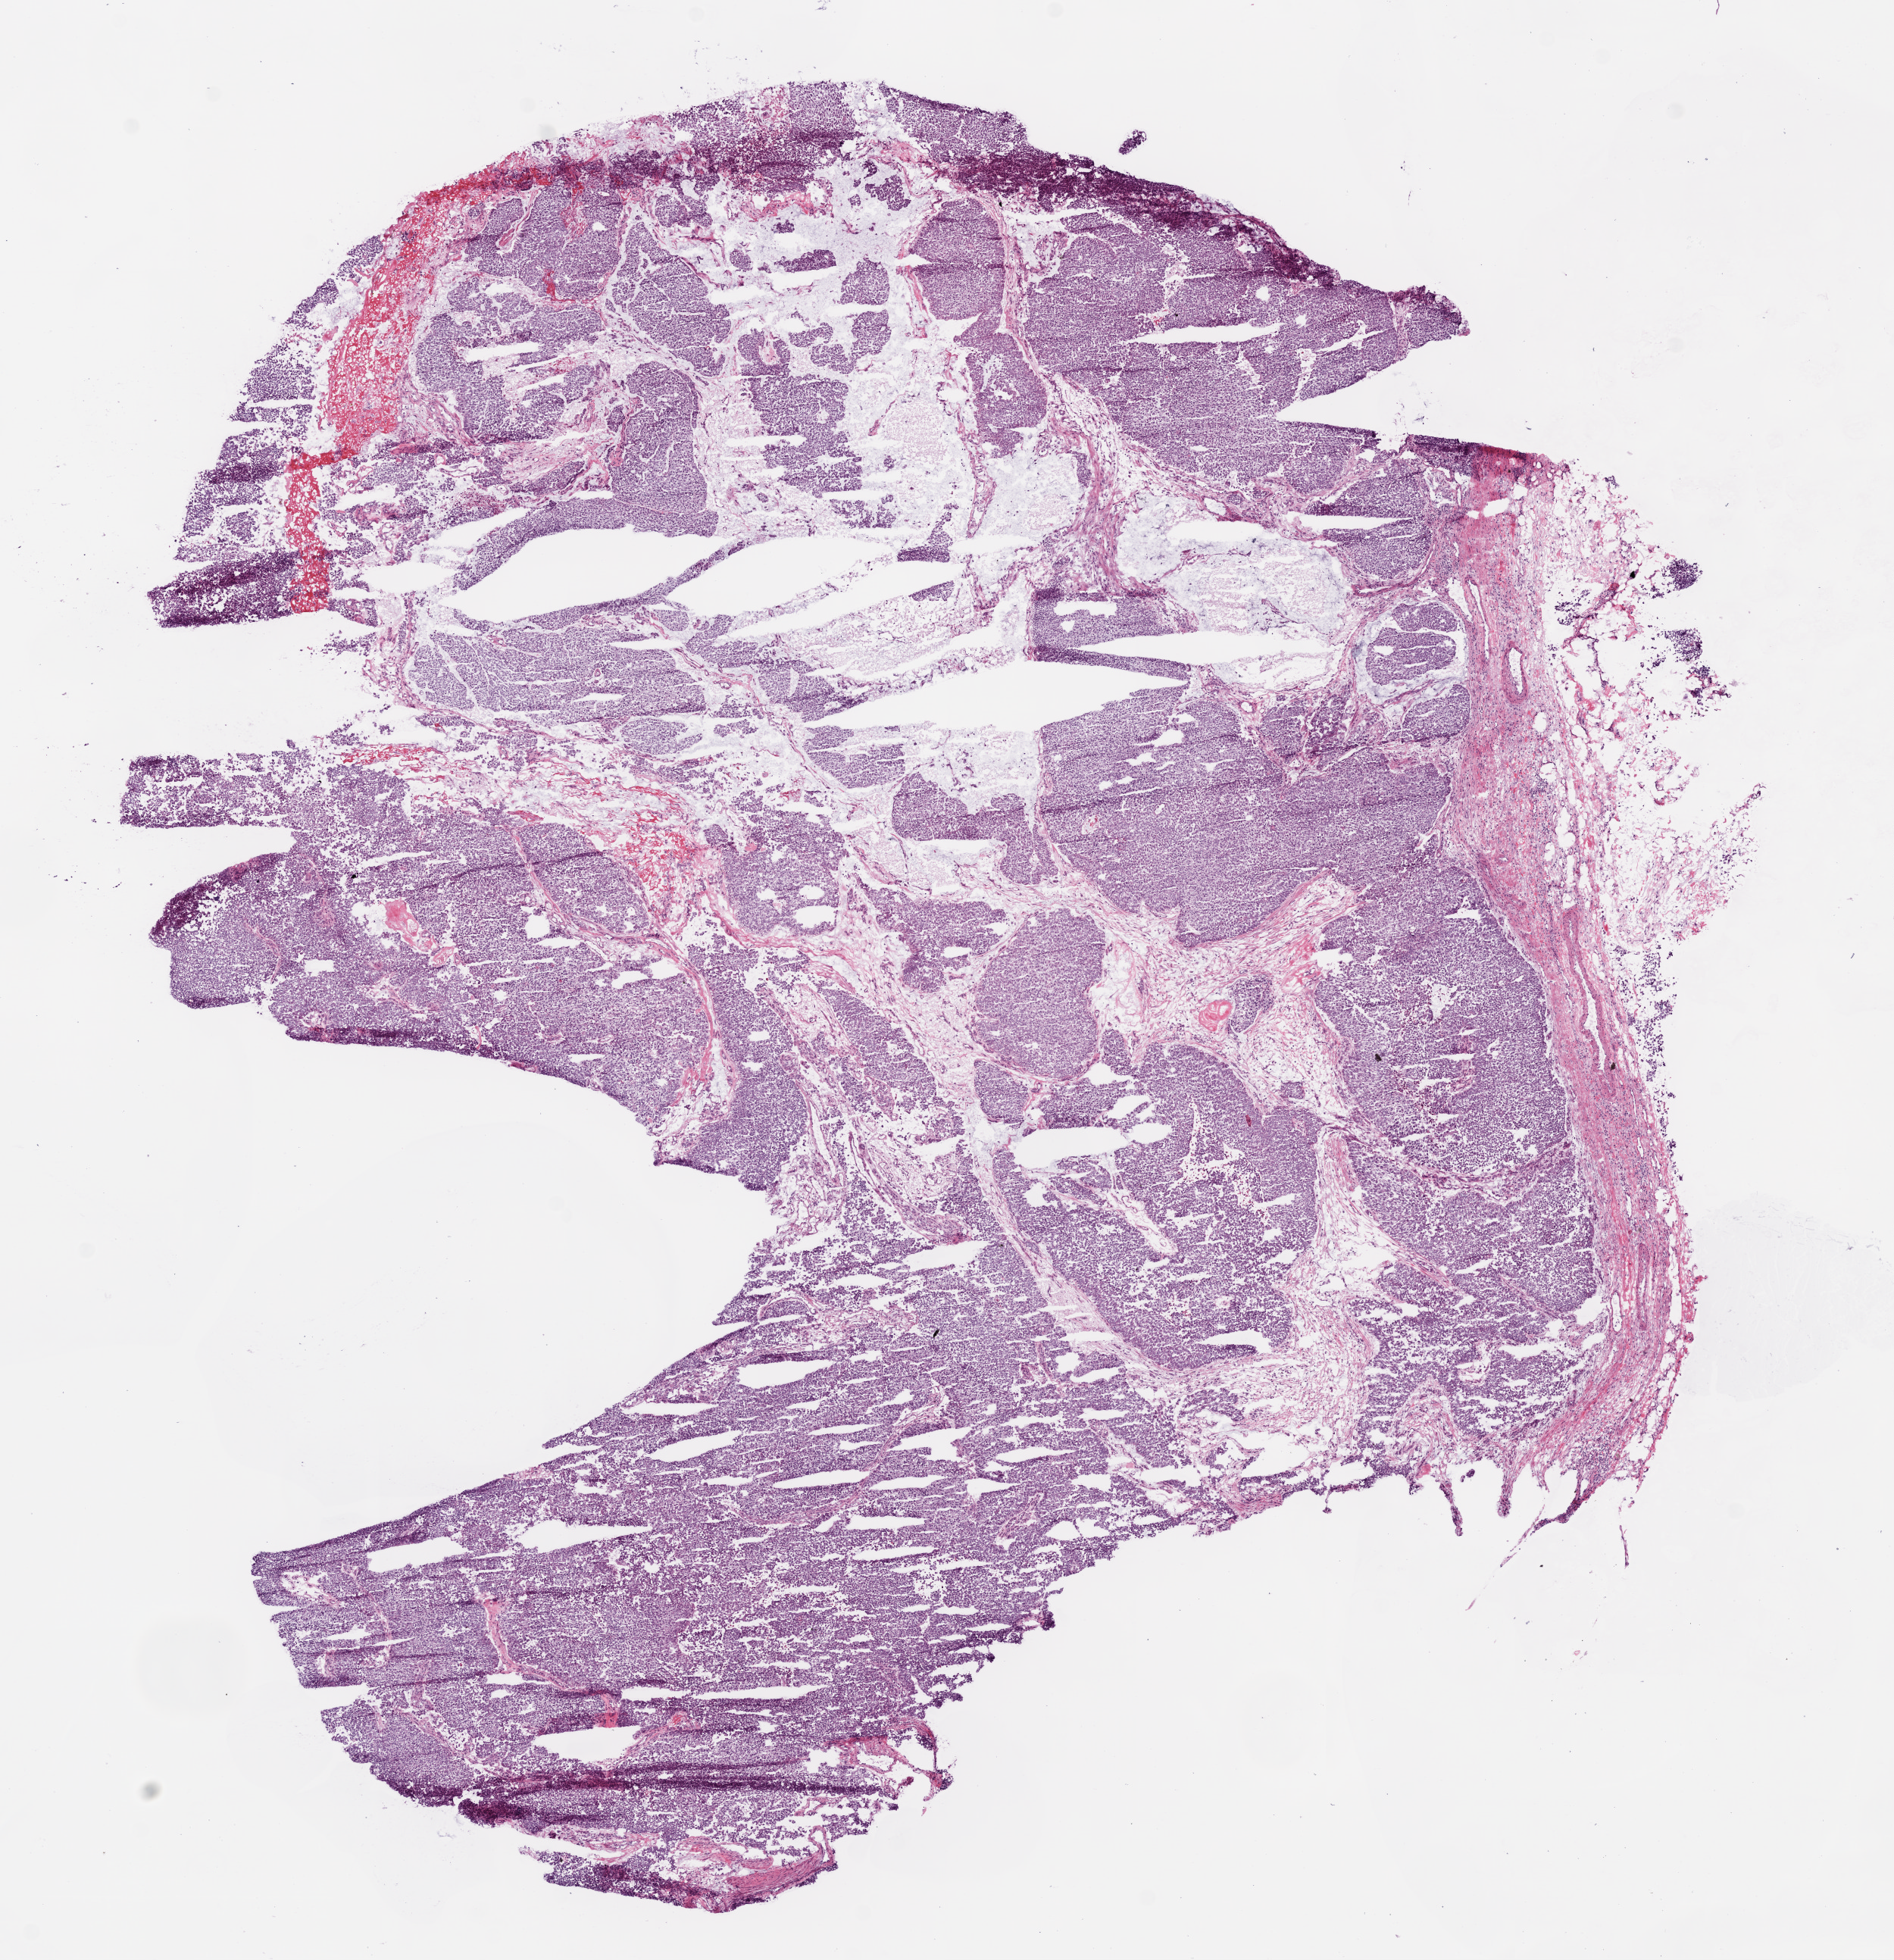
Digitized H&E tissue section (whole slide) — low-resolution overview of the scanned area, about 10.0 x 10.4 mm (from a 20x scan). Frozen section. Primary tumour sample from the kidney. Male, age 75 years at initial diagnosis. Composition of this section per pathologist review: tumour cells 85%, tumour nuclei 85%, normal cells 0%, stromal cells 5%, necrosis 10%.
- TNM: T2 NX M0
- AJCC pathologic stage: II
- laterality: right
- diagnosis: Papillary adenocarcinoma, NOS